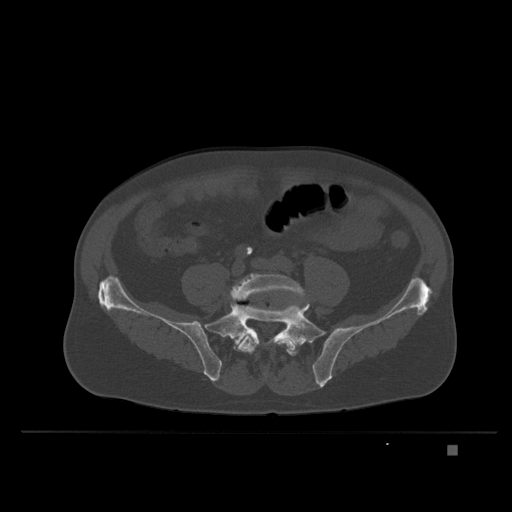
CT including the spine, one axial slice; slice 47 of 435 in the series (ordered by position); bone window (W 1800 / L 400 HU); 512 × 512 image matrix. Male patient, age 73 years. Case-level facts recorded for this patient, not image findings: primary cancer: skin.
Outlined on this slice (semi-automatically segmented with operator editing):
- L5 vertebra: bounding box (x1, y1, x2, y2) in pixels: (229, 274, 305, 356)